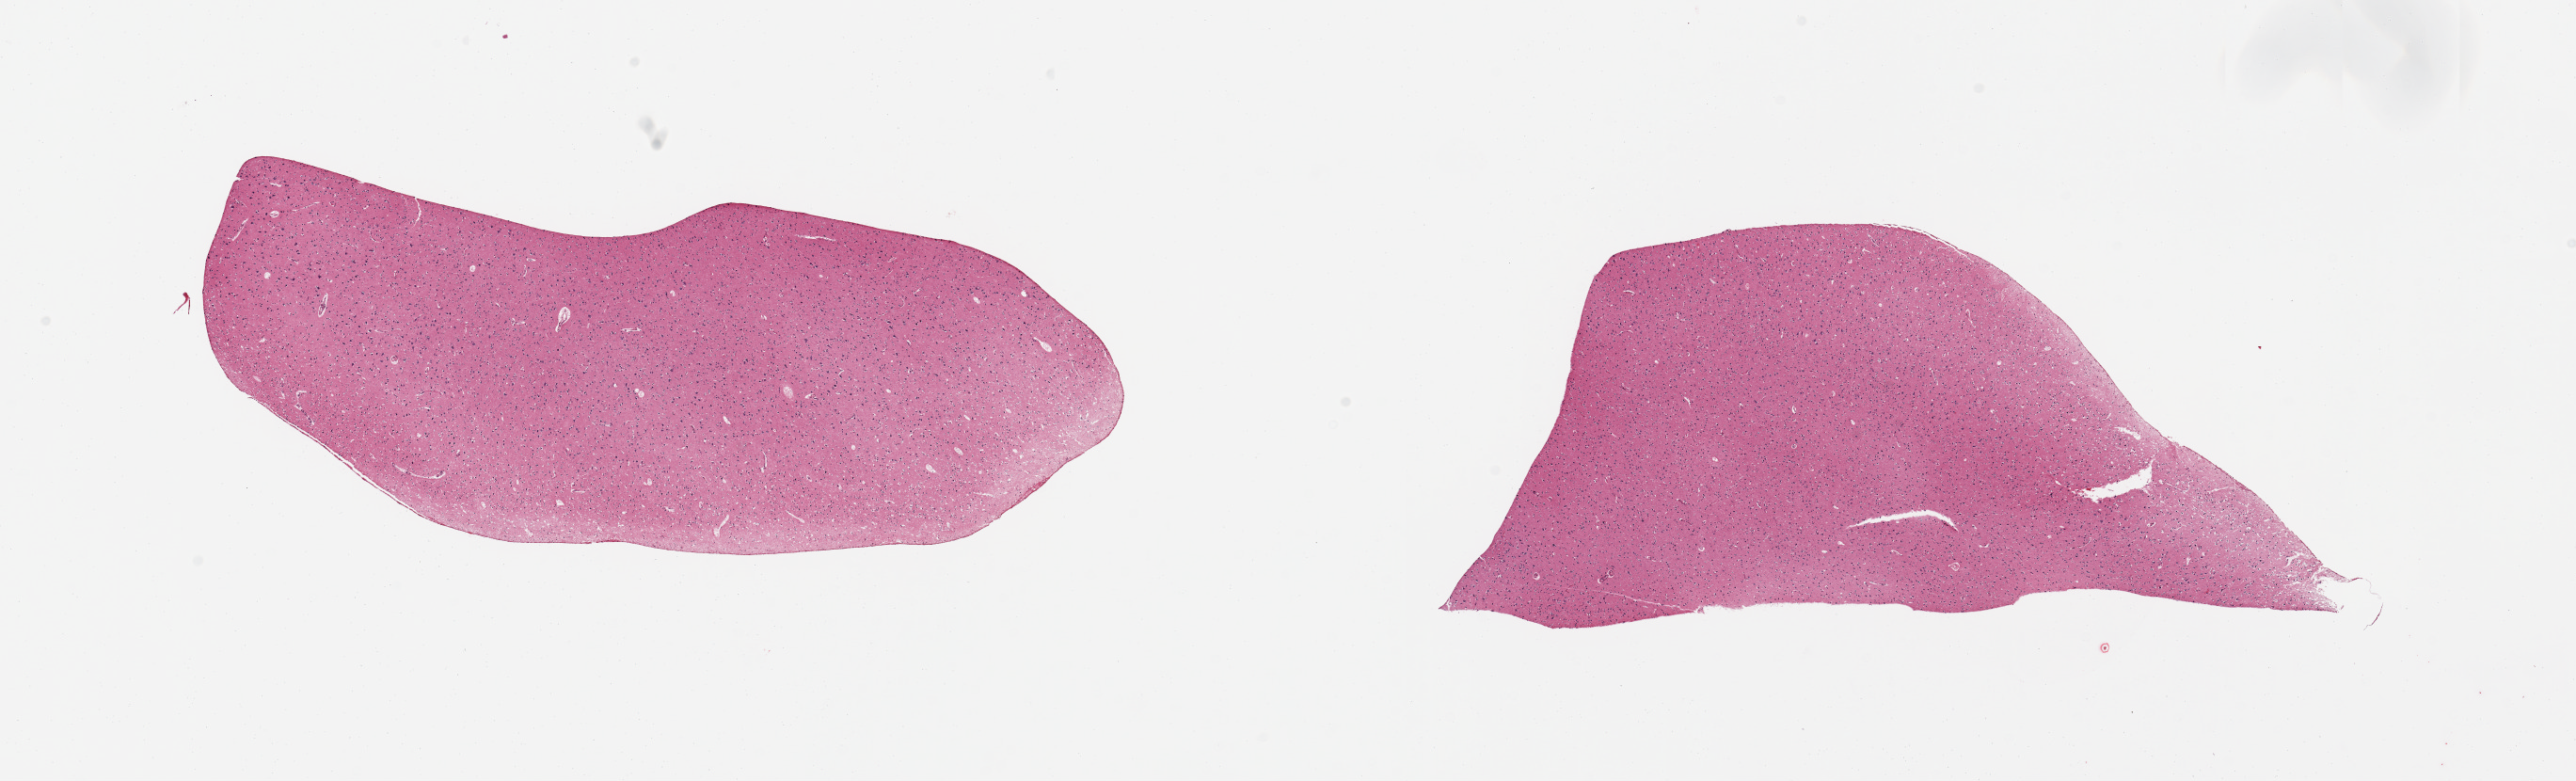
Digitized H&E-stained section, brightfield, whole scanned area (about 21.7 x 6.6 mm) shown as a low-resolution overview; PAXgene-fixed, paraffin-embedded tissue; target tissue: cerebral cortex; donor tissue sample. Donor: male.
Pathologist's review note for this sample: 2 pieces.